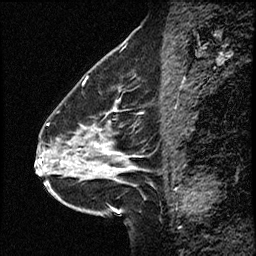
Breast MRI (dynamic contrast-enhanced), one sagittal slice; slice 24 of 50 in the series (ordered by position); dynamic contrast-enhanced study with each time point stored as its own series, time point 2 of 4 at this slice position (early post-contrast, ordered by acquisition time); 1.5 T; TE 4.2 ms, TR 17.5 ms; 3 mm slice thickness; 256 × 256 image matrix, field of view 200 × 200 mm. From the clinical record (not read from this slice): setting: breast cancer imaged before/during neoadjuvant chemotherapy.
Outlined on this slice (semi-automatic segmentation, software-assisted and operator-edited):
- analysis volume of interest (the breast-tissue region the enhancement analysis was run in; not a lesion): bounding box <52,98,156,207> (left, top, right, bottom; pixels)
- tumour enhancement mask (voxels above the 100 % enhancement threshold inside the analysis volume of interest): <96,145,119,171>